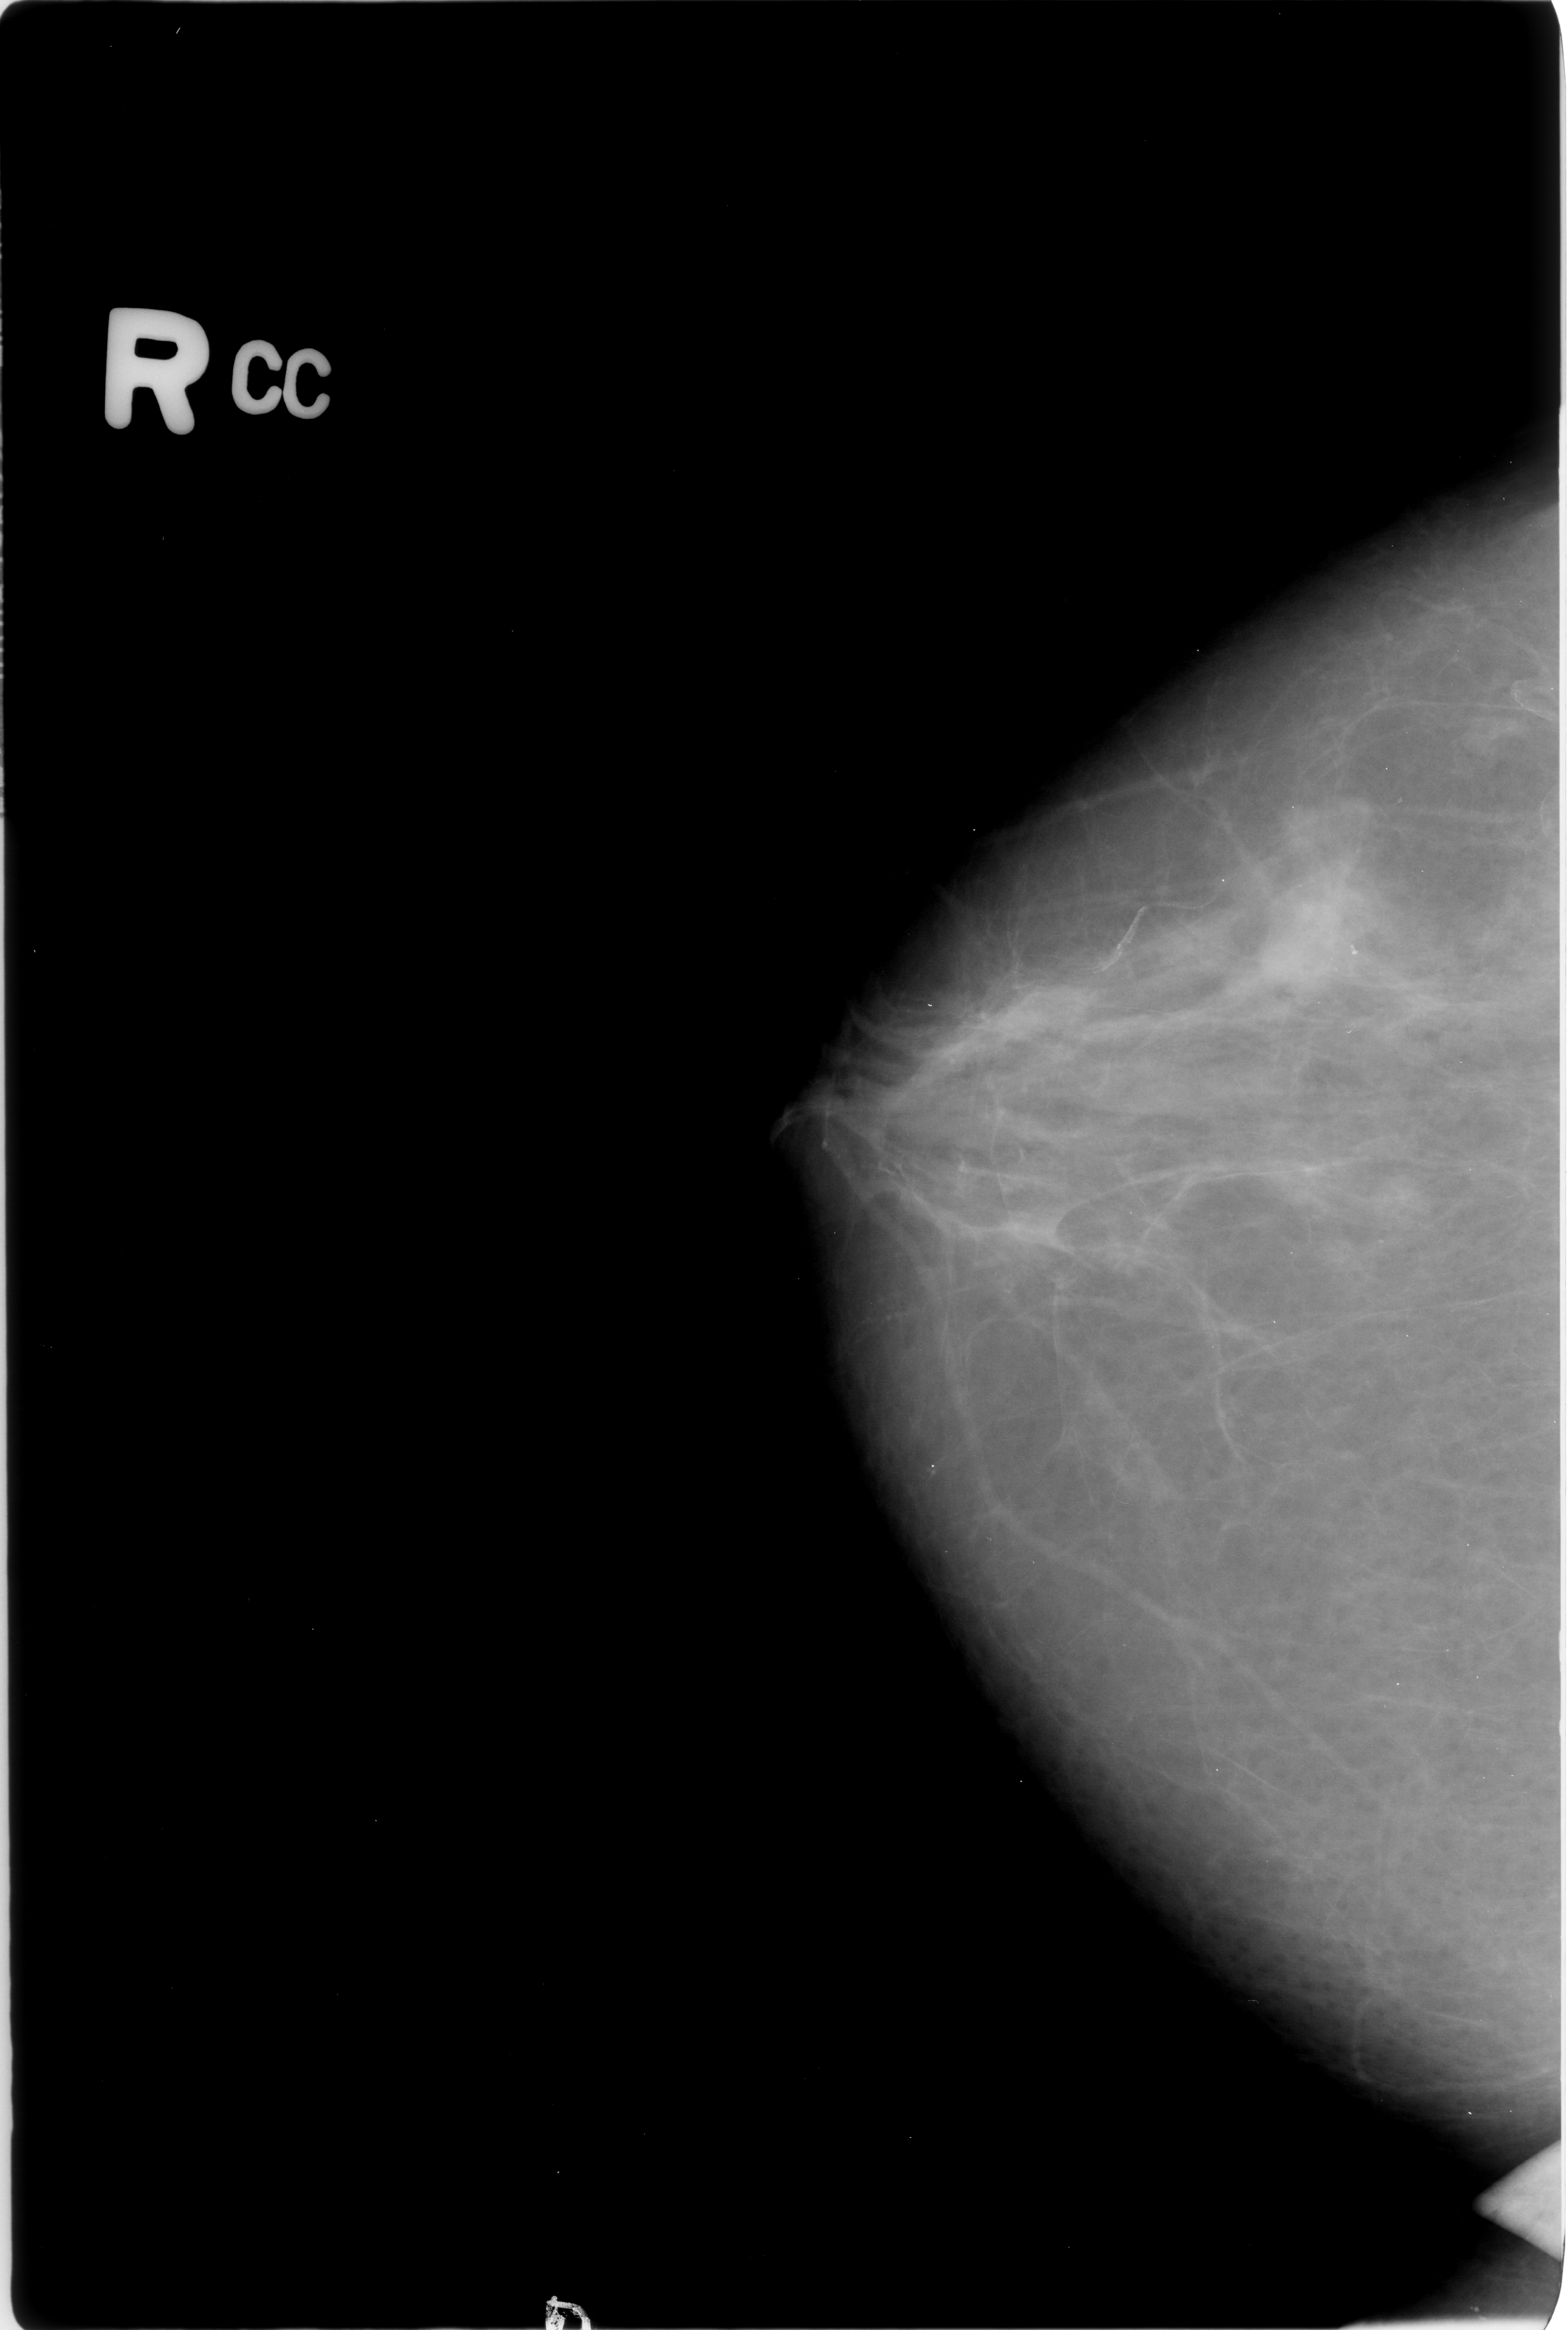
Digitized screen-film mammogram; right breast; craniocaudal (CC) view; 1568 × 2330 image matrix.
Marked abnormalities (boxes around the expert regions of interest):
- mass, shape lobulated, margins obscured / ill defined; BI-RADS assessment category 3; pathology result (as recorded, not read from the image): malignant: bounding box (x1, y1, x2, y2) in pixels: (1230, 862, 1384, 1008)